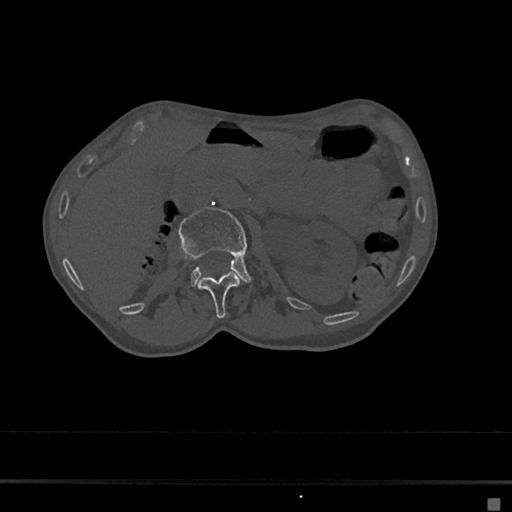
CT including the spine, one axial slice; slice 45 of 797 in the series (ordered by position); 120 kVp; bone window (W 1800 / L 400 HU); 0.5 mm slice thickness; 512 × 512 image matrix, field of view 360 × 360 mm. Female patient, age 68 years. From the clinical record (not read from this slice): primary cancer: renal.
Structures marked on this image (semi-automatic segmentation, software-assisted and operator-edited):
- L1 vertebra: bounding box [x1, y1, x2, y2] px = [198, 273, 240, 319]
- L2 vertebra: [179, 207, 251, 286]